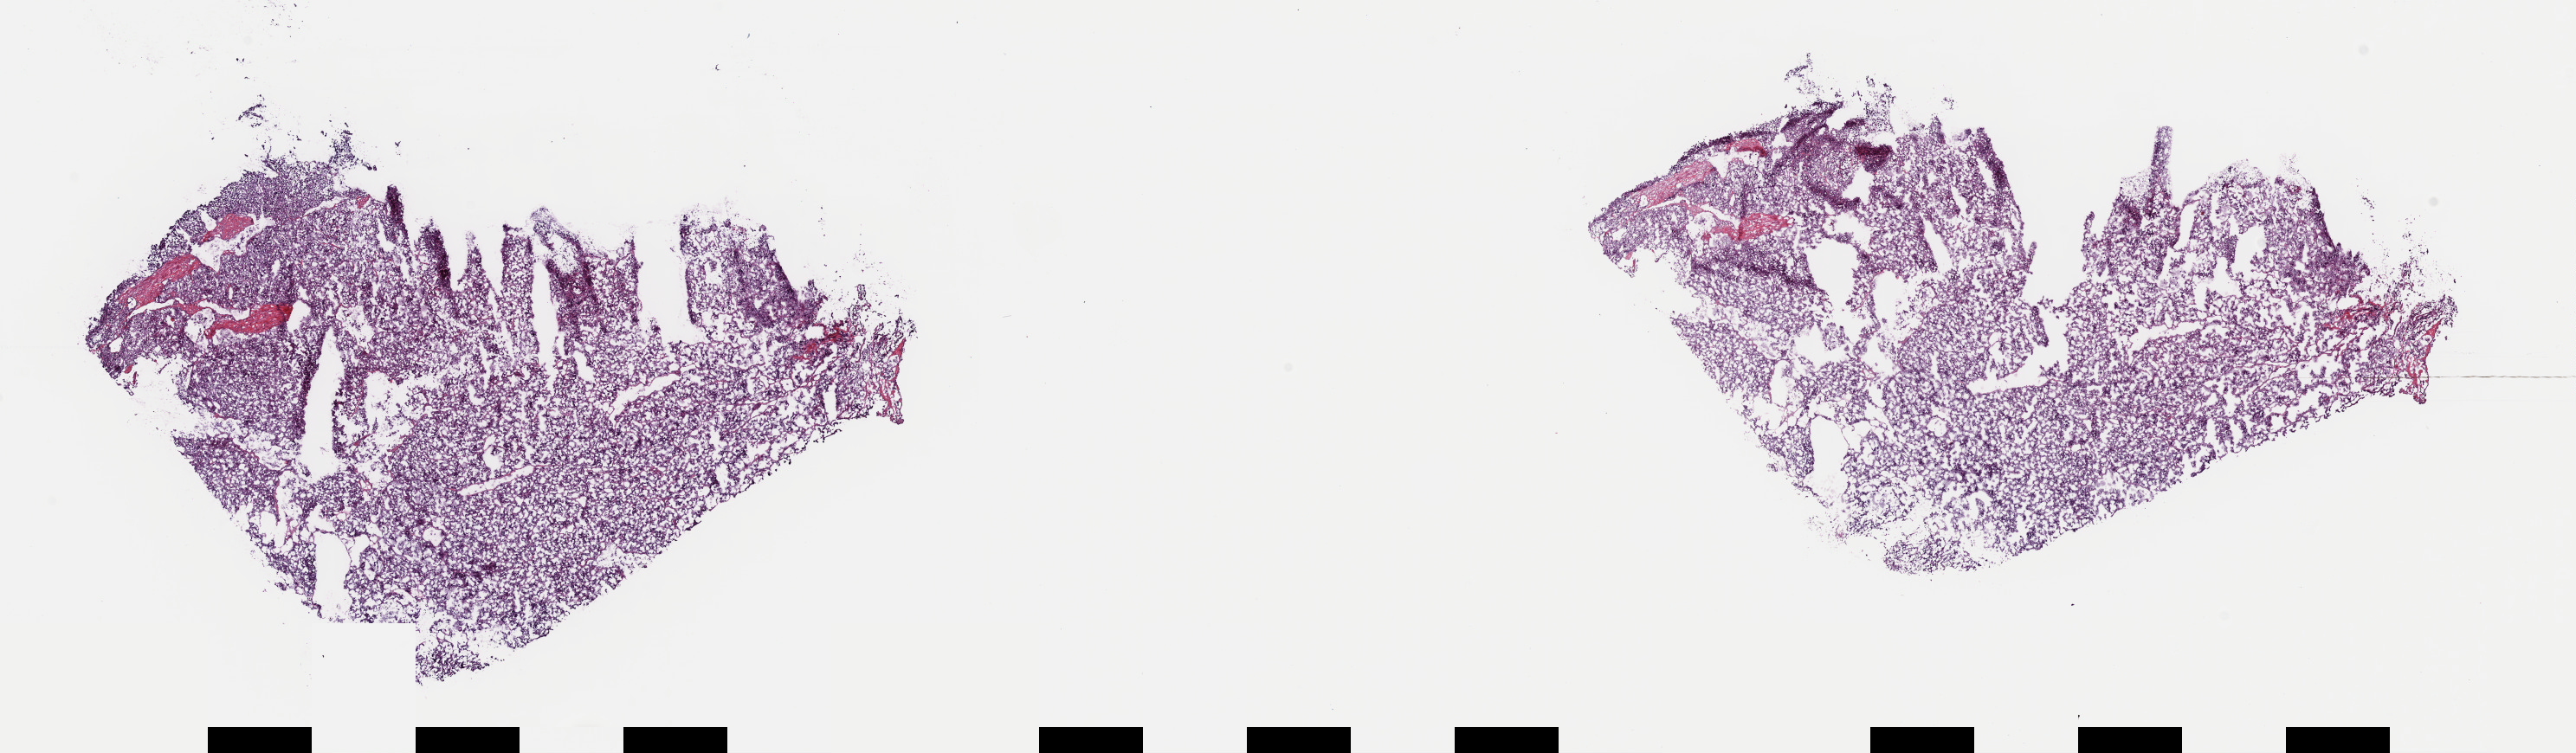
H&E whole-slide image — whole scanned area (about 23.5 x 6.9 mm, slide scanned at 40x) shown as a low-resolution overview, frozen section from the top of the tissue portion, primary tumour sample. Male patient; age at initial diagnosis 33 years. Composition of this section per pathologist review: tumour cells 90%, tumour nuclei 100%, normal cells 0%, stromal cells 10%, necrosis 0%. Inflammatory infiltration, as recorded: lymphocyte infiltration 0%, monocyte infiltration 0%, neutrophil infiltration 0%.
Histologic diagnosis: Extra-adrenal paraganglioma, NOS (thorax, NOS).